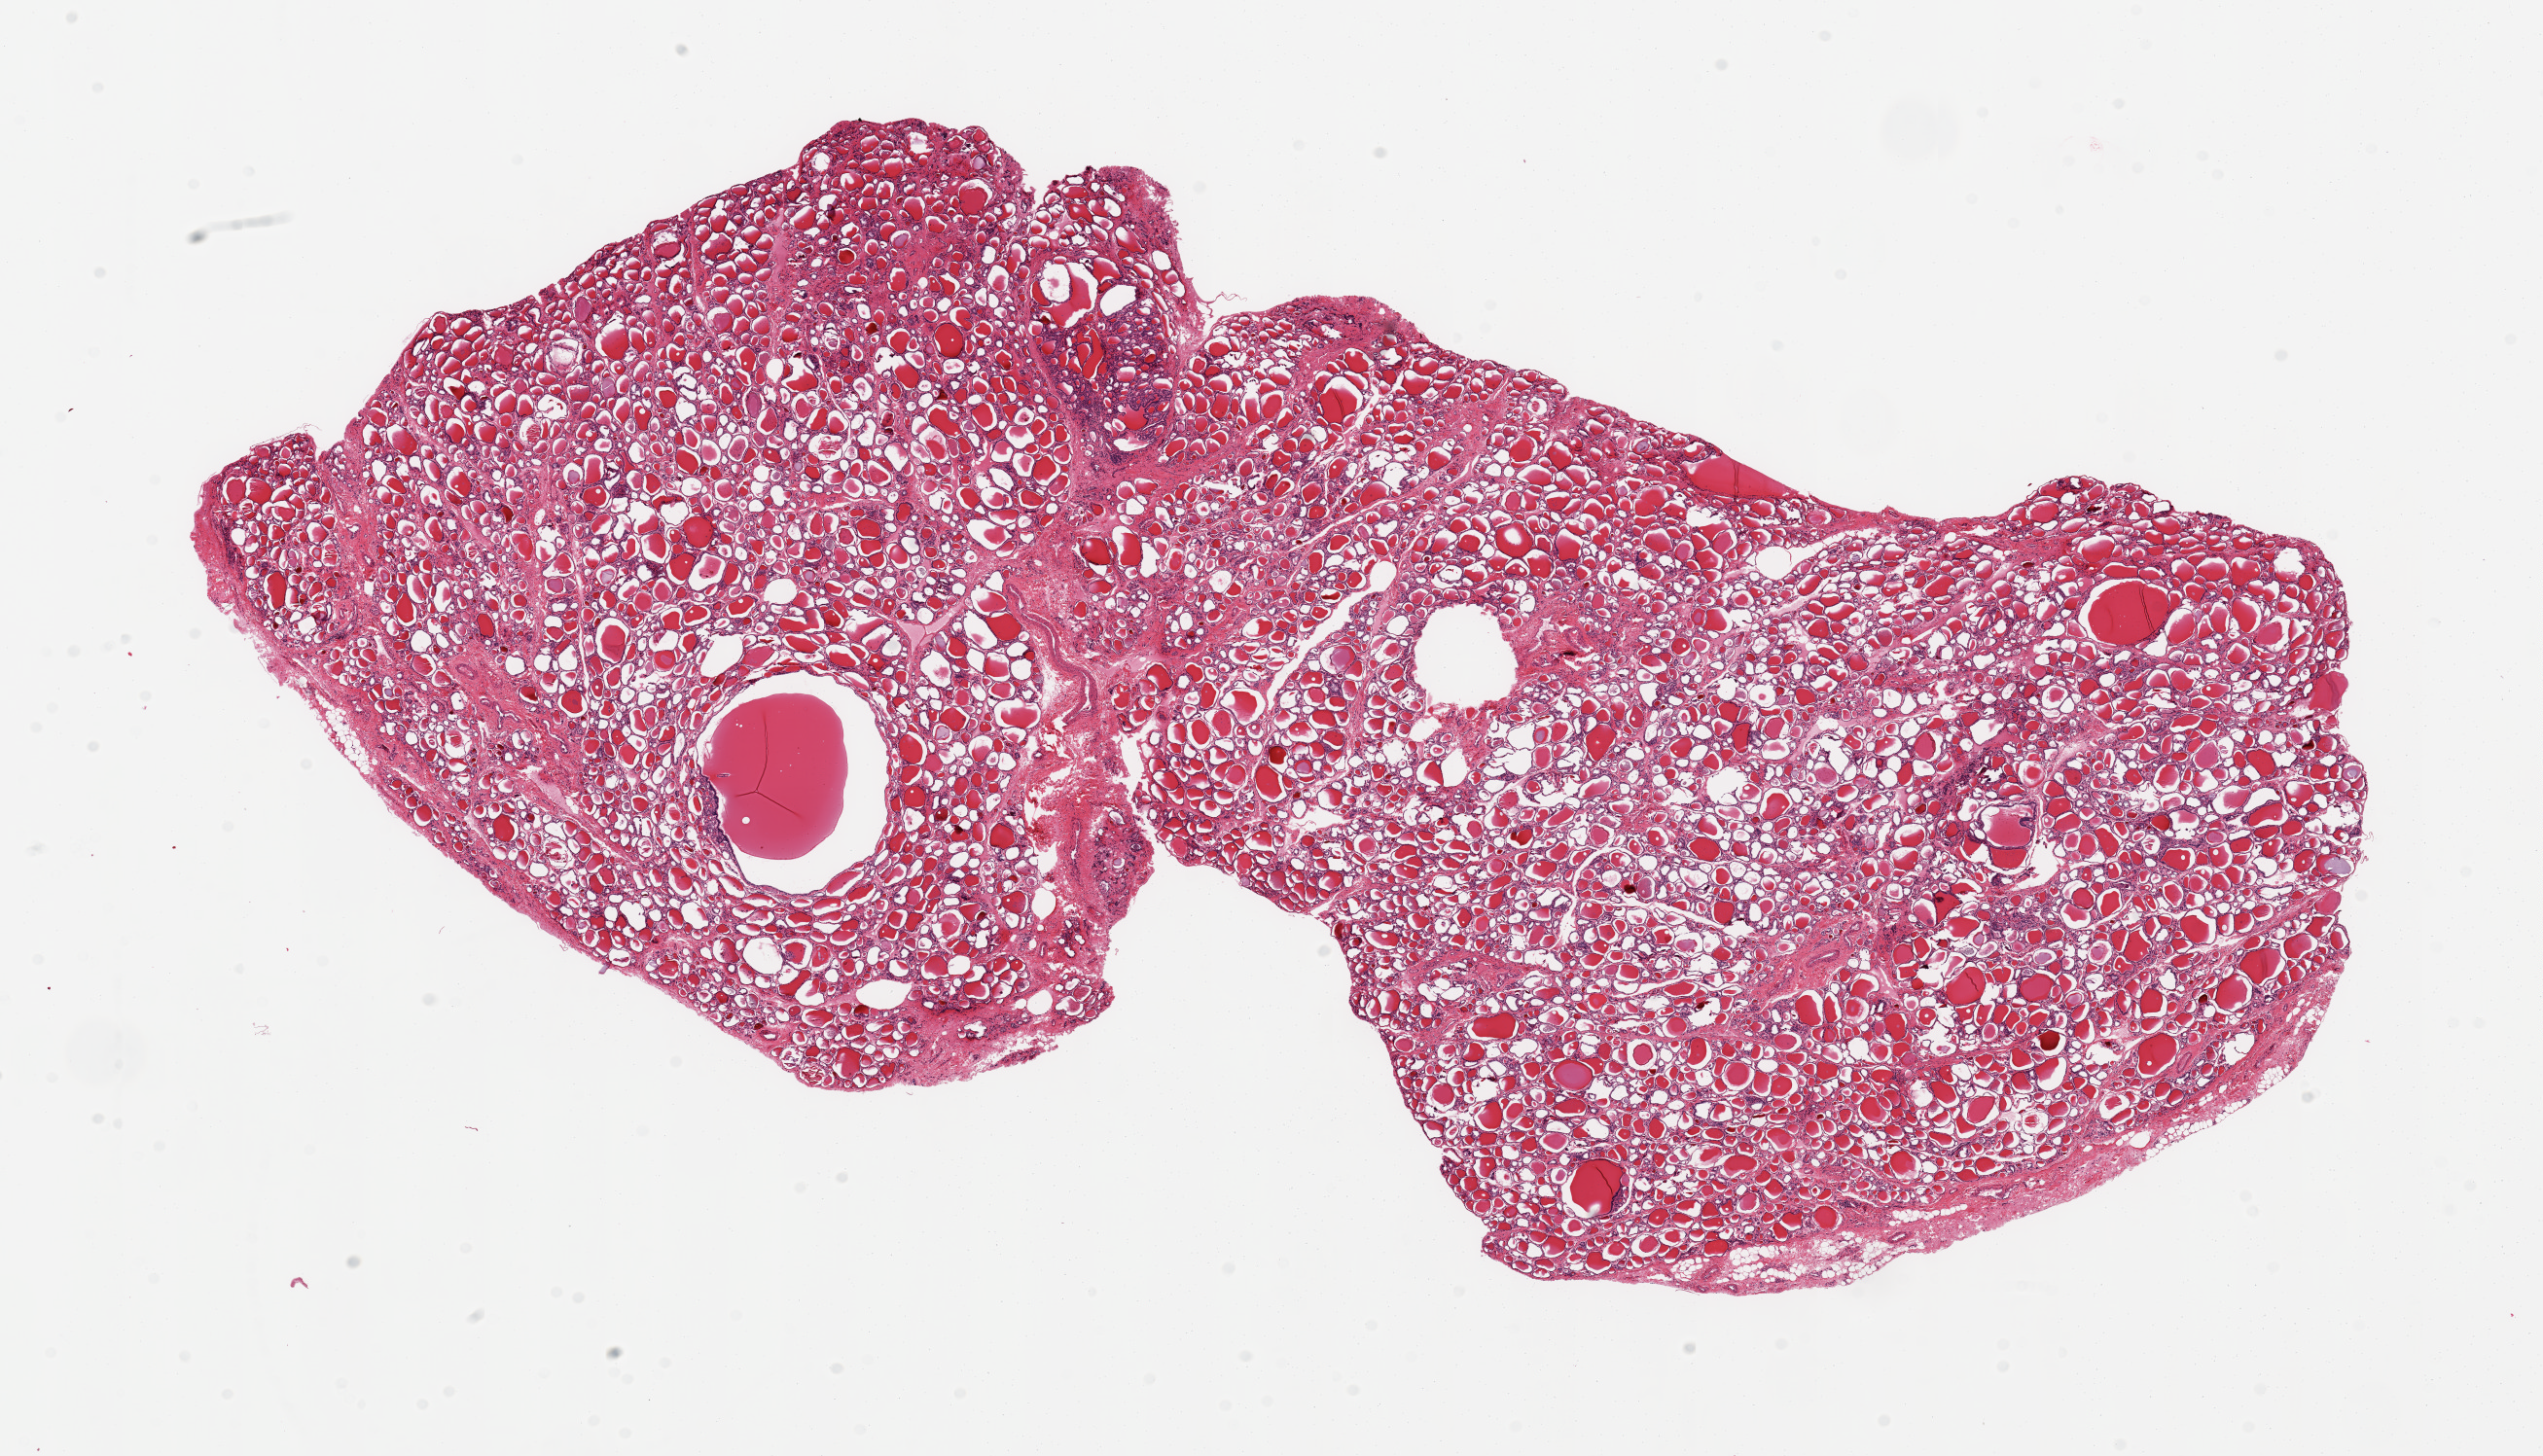
Haematoxylin and eosin whole-slide image — a low-resolution overview of the entire scanned area, about 20.7 x 11.8 mm; PAXgene-fixed paraffin-embedded (PFPE) section; target tissue: thyroid; tissue donor sample. Donor sex: female.
Reviewer comment on this tissue sample: 16.7x7.1mm. 1.8mm colloid cyst.